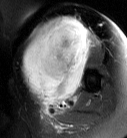
MRI of an extremity soft-tissue mass, one axial slice; slice 48 of 87 in the series (ordered by position); T2-weighted fat-saturated; MR volume resampled by the dataset authors to the PET/CT grid (not the native acquisition matrix); 127 × 138 image matrix. Female patient. From the clinical record (not read from this slice): histological type: pleiomorphic leiomyosarcoma; grade: high; site of the primary tumour: left biceps.
Annotated regions visible in this slice (expert contour drawn on MRI and transferred to this co-registered scan by the dataset authors):
- gross tumour volume including surrounding oedema: bounding box (x1, y1, x2, y2) in pixels: (22, 16, 96, 111)
- gross tumour volume (mass): (22, 16, 92, 104)